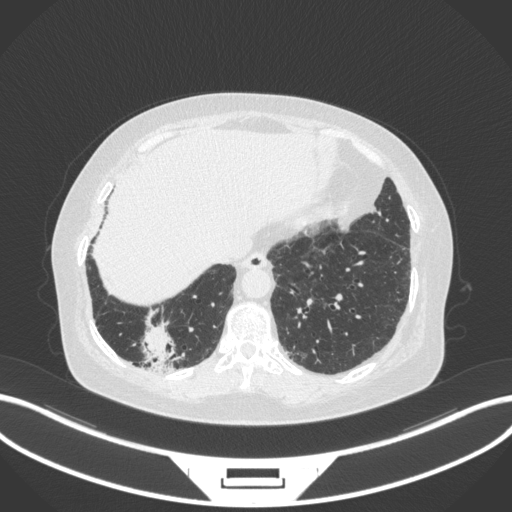
Chest CT, one axial slice; slice 32 of 303 in the series (ordered by position); 120 kVp; lung window (W 1500 / L -600 HU); 1 mm slice thickness; 512 × 512 image matrix, field of view 400 × 400 mm. Female patient, age 65 years. From the clinical record (not read from this slice): clinical TNM (as recorded): T2b N1 M0.
Annotated regions visible in this slice (rectangle marked by the reading radiologist):
- lung tumour (recorded histology: adenocarcinoma): bounding box <132,311,180,376> (left, top, right, bottom; pixels)